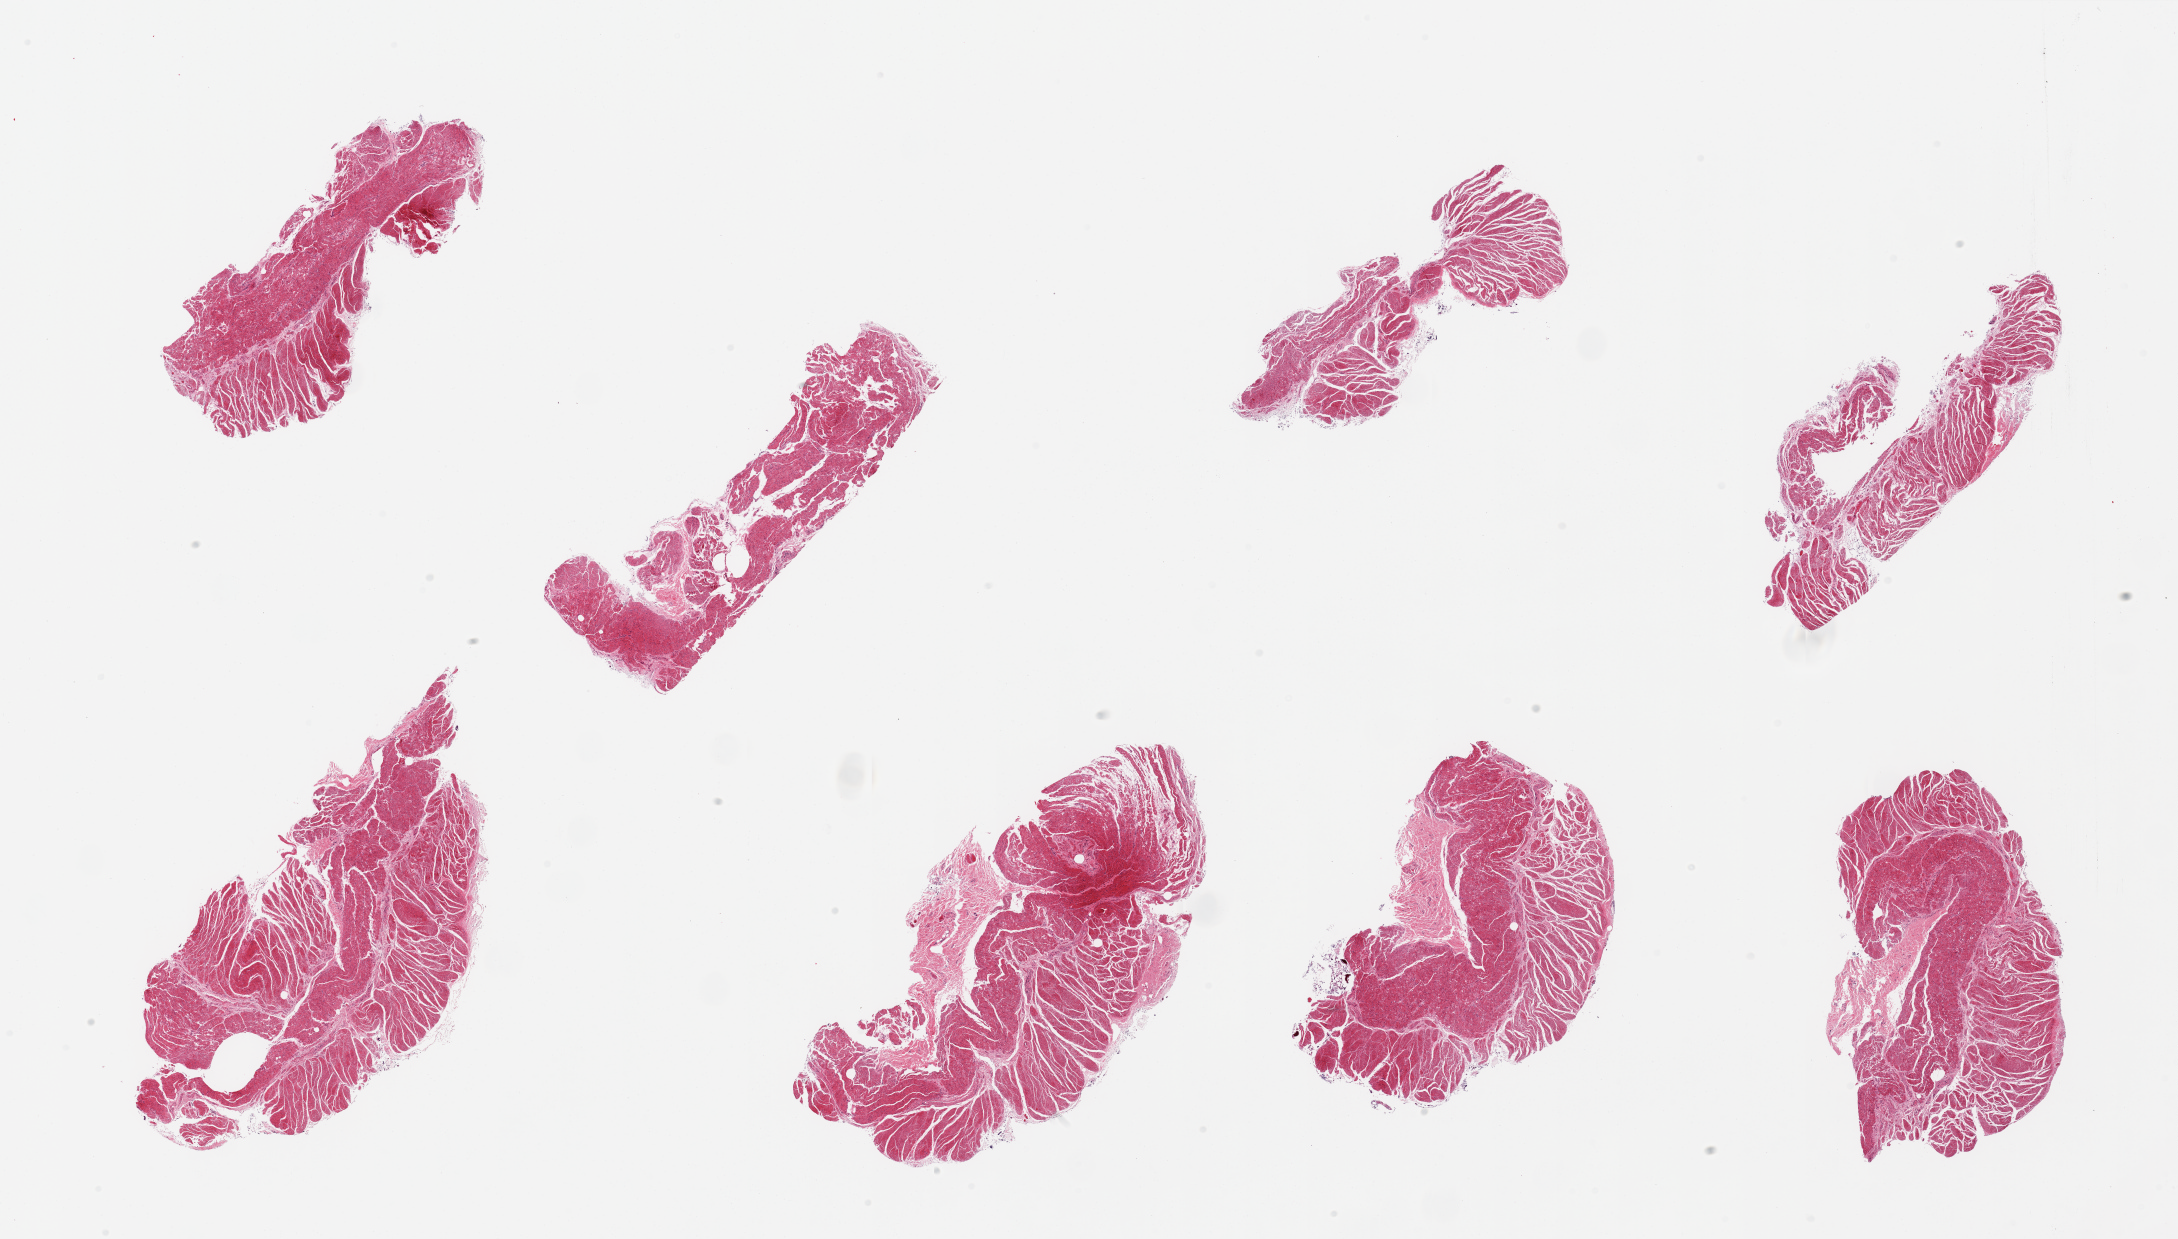
Hematoxylin and eosin (H&E) whole-slide image — low-resolution overview of the scanned area, about 34.5 x 19.6 mm. PAXgene-fixed, paraffin-embedded tissue. Target tissue: esophageal muscle. Donor tissue sample. Donor: male.
• pathologist's review note for this sample: 6 pieces muscularis, good specimens